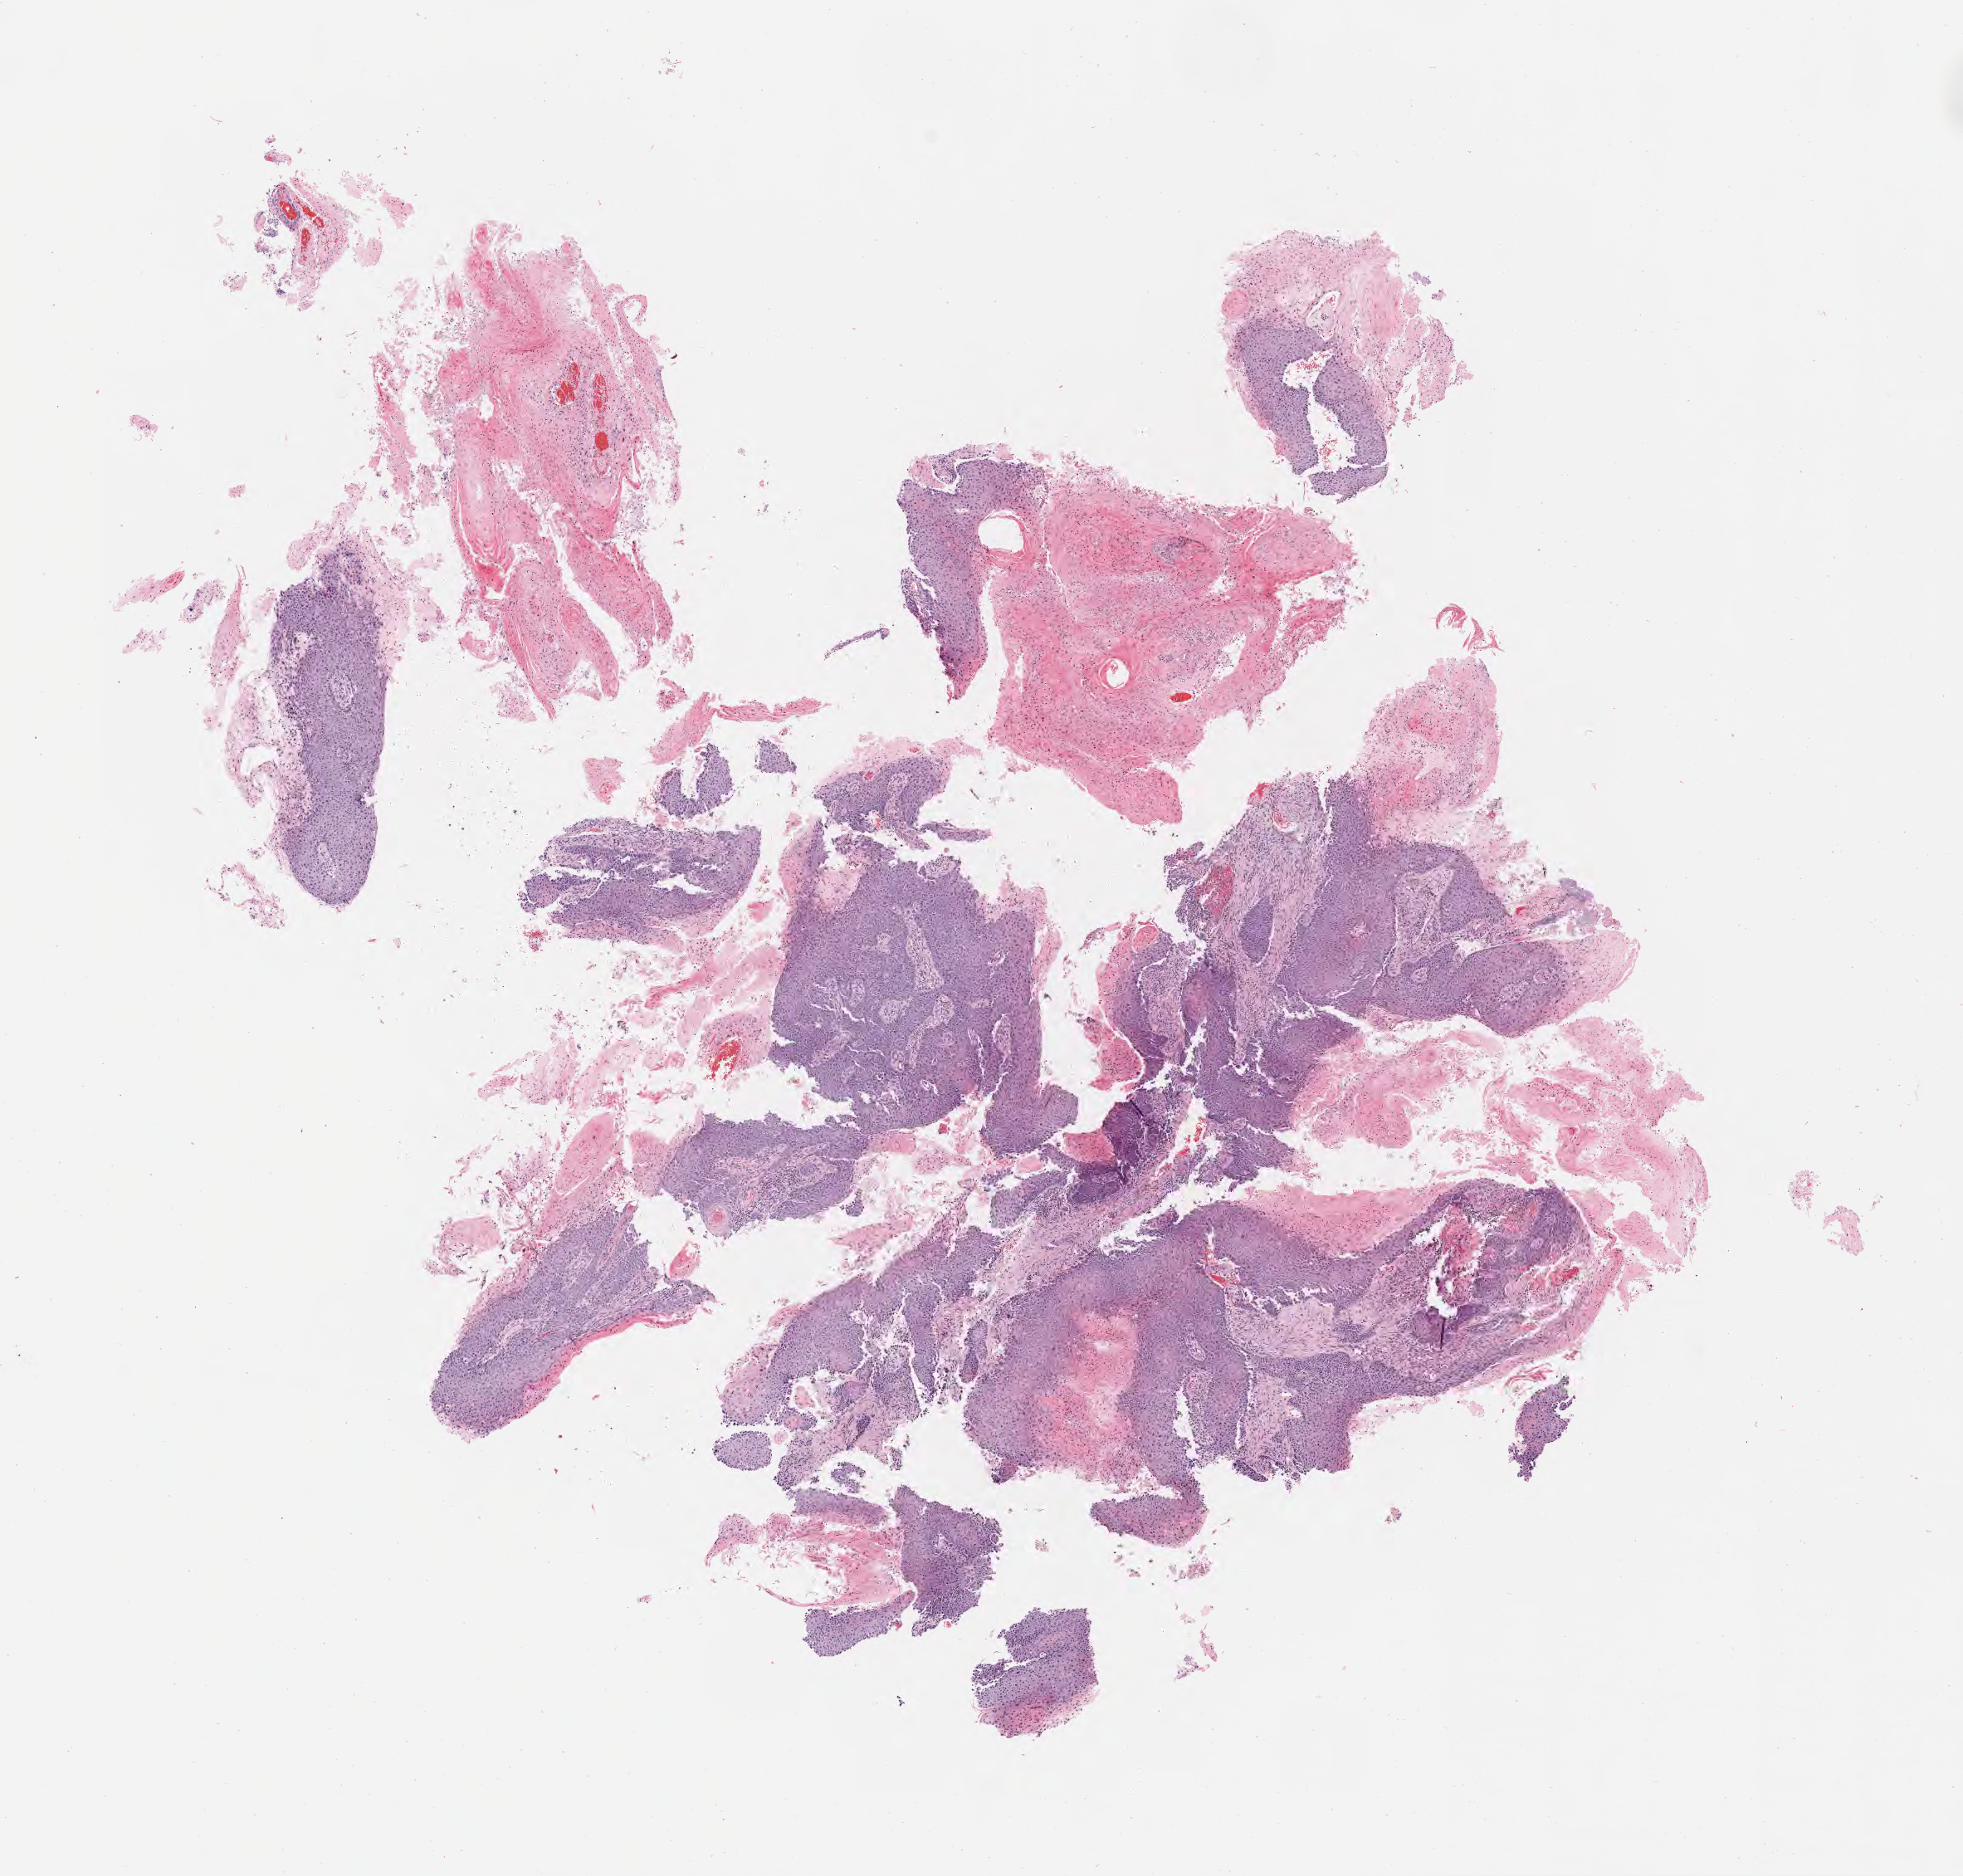
Whole-slide image, haematoxylin and eosin stain — whole scanned area (about 9.6 x 9.1 mm) shown as a low-resolution overview, specimen: tumor tissue, anatomic site: cervix. Female patient, aged 42.
Histologic diagnosis: Squamous cell carcinoma, keratinizing, NOS.